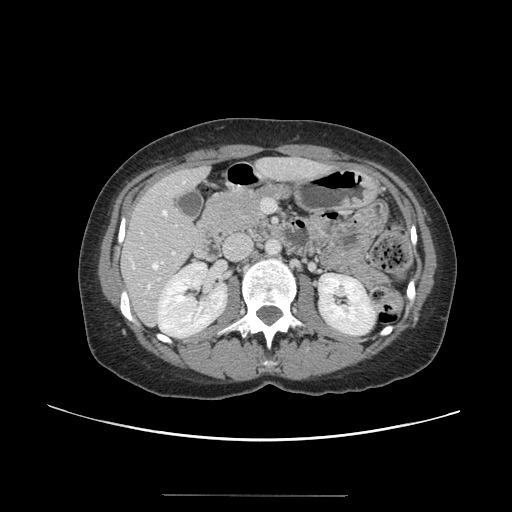
Contrast-enhanced abdominal CT, one axial slice; position 60 of 144 along the scan axis; 120 kVp; soft-tissue window (W 400 / L 40 HU); 2.5 mm slice thickness; 512 × 512 image matrix, field of view 380 × 380 mm. Female patient, age 53 years. From the clinical record (not read from this slice): diagnosis: colorectal cancer liver metastases, imaged before liver resection; multiple liver metastases: yes; largest metastasis: 1.1 cm; disease in both lobes: no.
Annotated regions visible in this slice (outlined manually by an expert reader):
- hepatic veins: bounding box <148,210,167,288> (left, top, right, bottom; pixels)
- liver: <123,159,326,324>
- planned liver remnant (the part of the liver to remain after resection): <123,159,325,309>
- portal vein (with intrahepatic branches): <157,252,175,281>